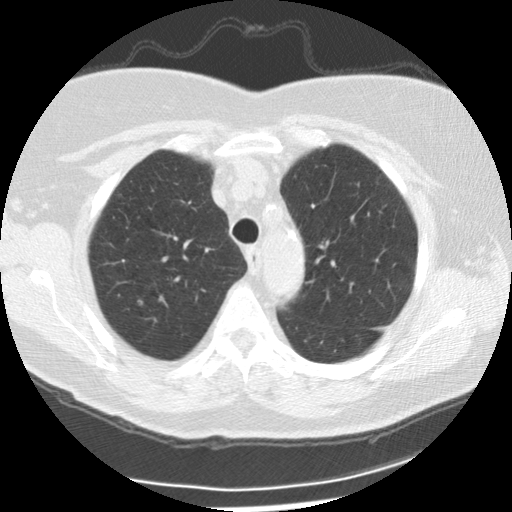
Chest CT (low-dose screening protocol), one axial image. Baseline screening round. Lung window (W 1500 / L -600 HU). 2.5 mm slice thickness. Slice 51 of 225 in the series. 512 × 512 image matrix. Female, age 72 years at enrolment. Current smoker at enrolment.
Expert reader's lesion annotation, bounding box (x1, y1, x2, y2) in pixels: (124, 294, 150, 316). Screening reader's record for this exam: no non-calcified nodule ≥4 mm recorded. Official screen result: negative screen, minor abnormalities not suspicious for lung cancer.